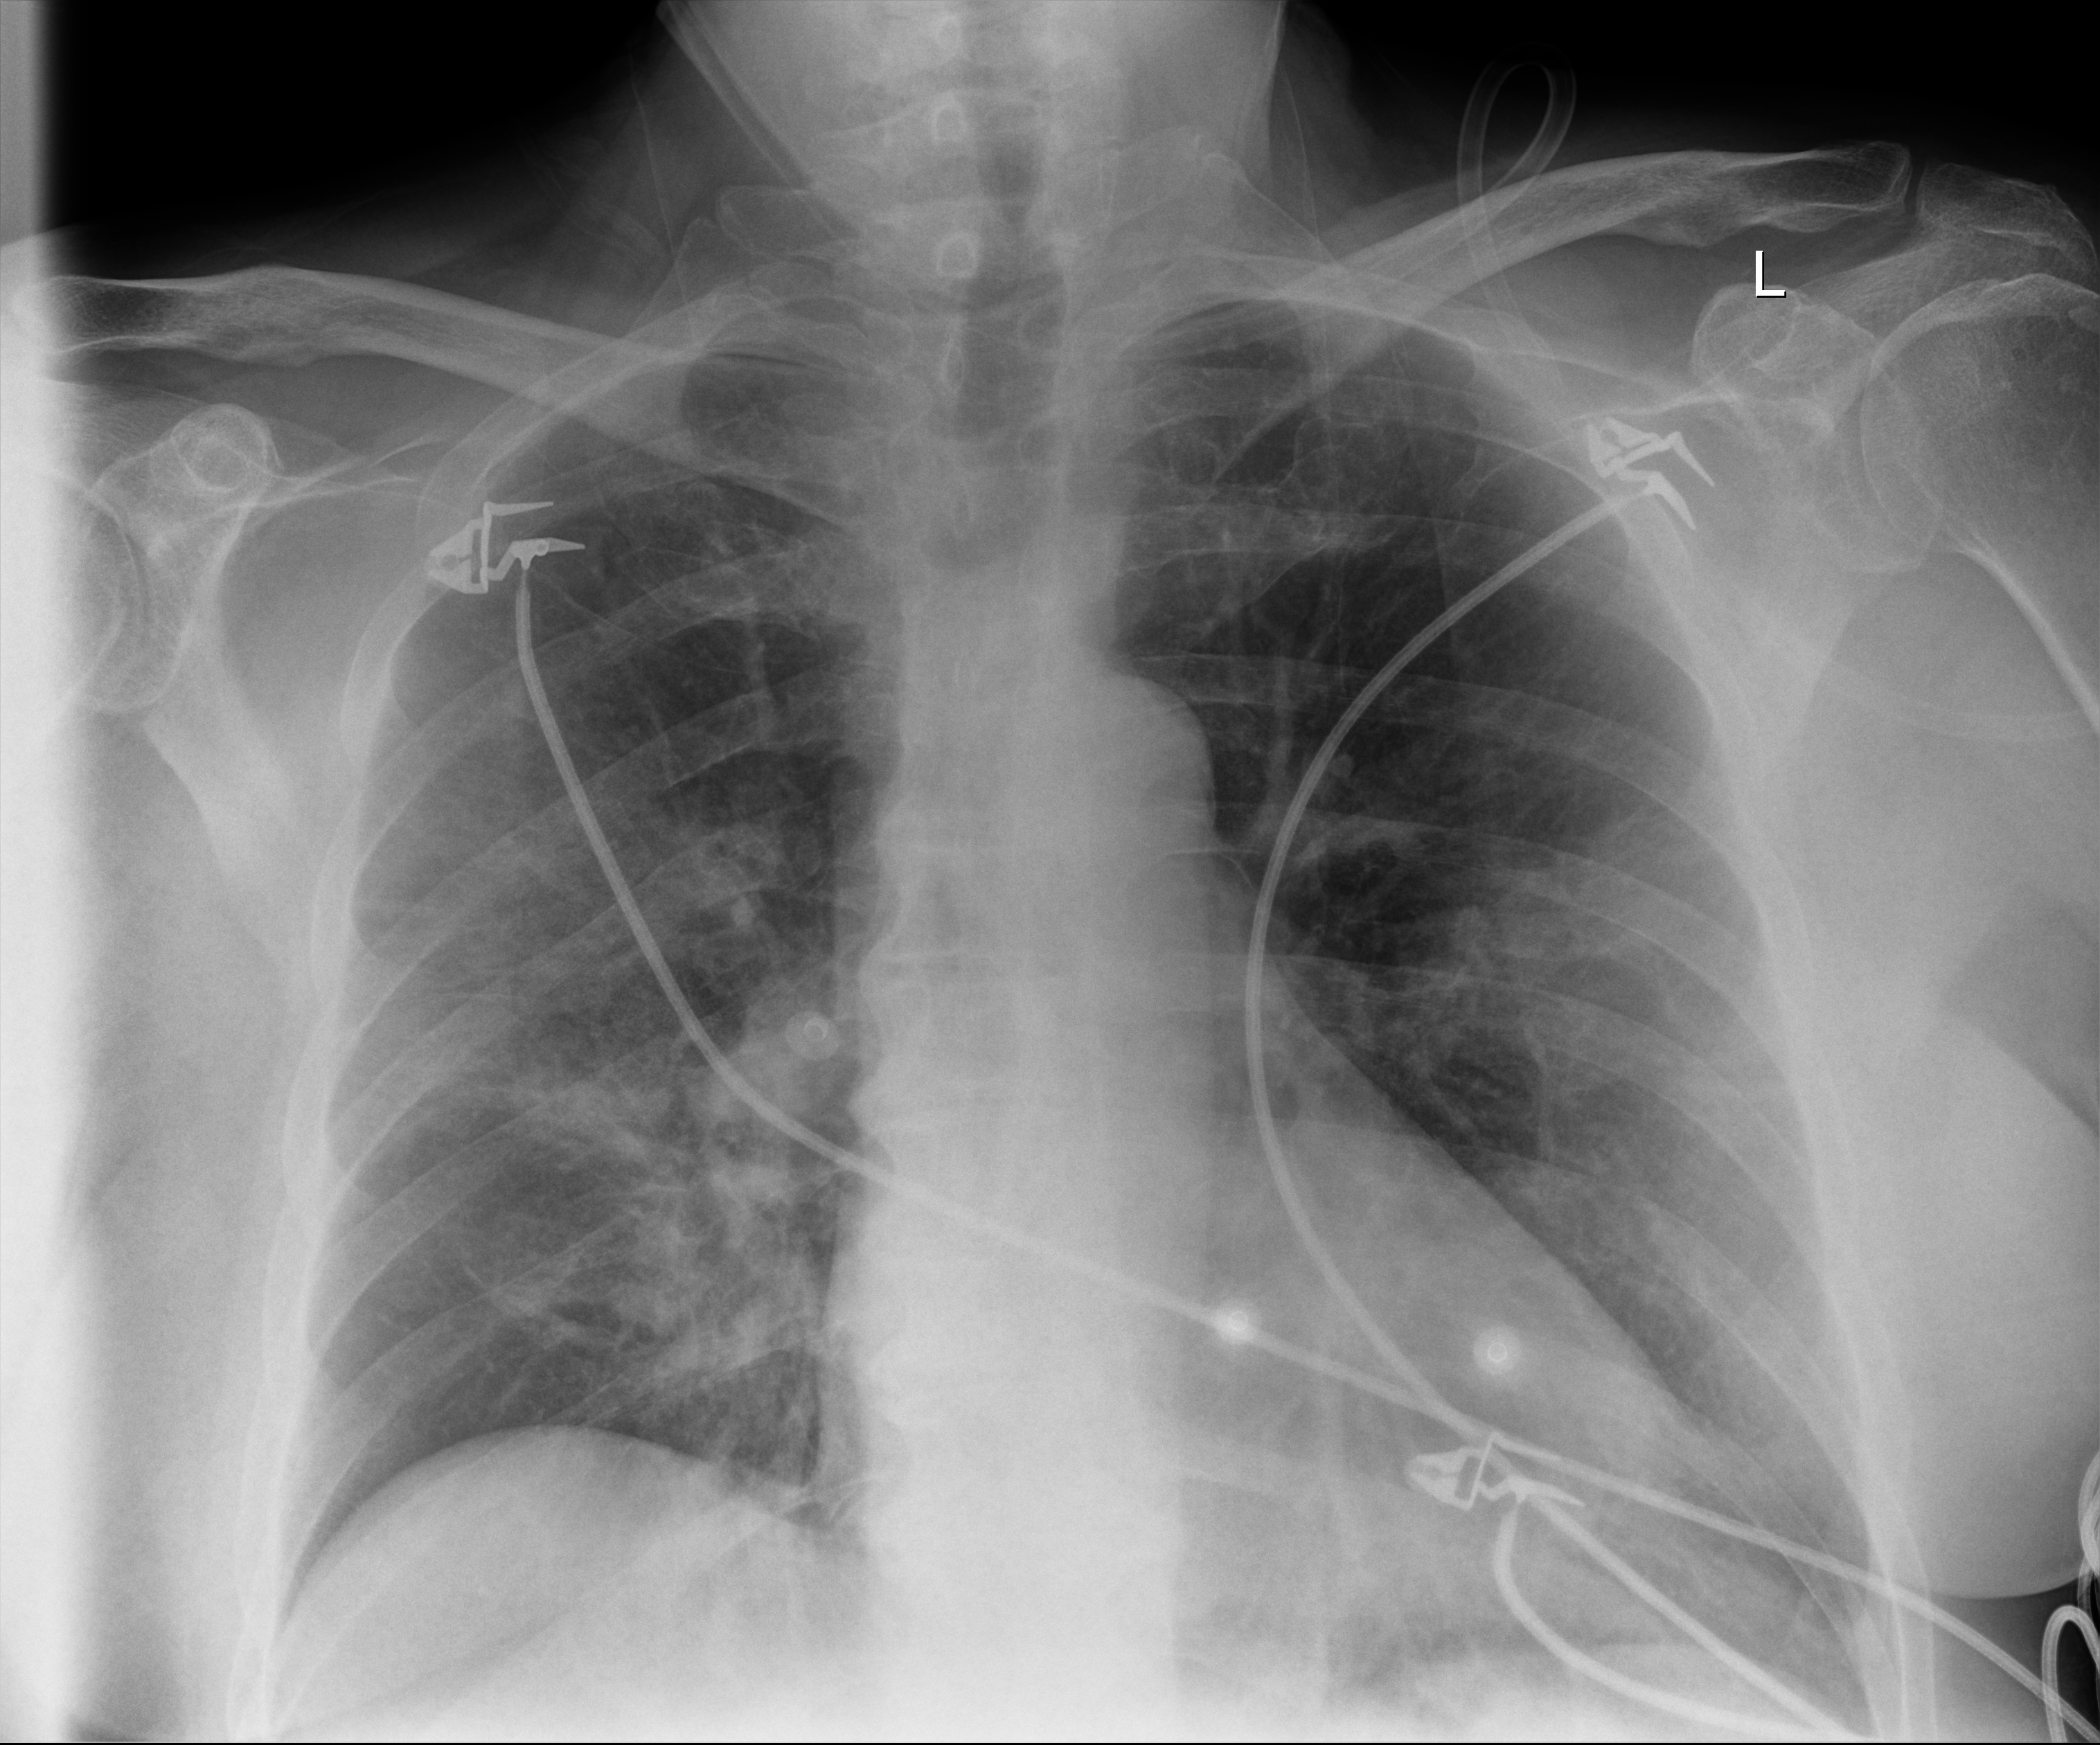
Portable chest radiograph; anteroposterior (AP) projection. Patient hospitalised with COVID-19; male, aged 60–74 years.
Admission-level facts for this patient (not findings on this image; timing relative to this image not recorded): mechanically ventilated during this hospital stay: no; chronic kidney disease (admission record): no; admitted to intensive care during this hospital stay: no.